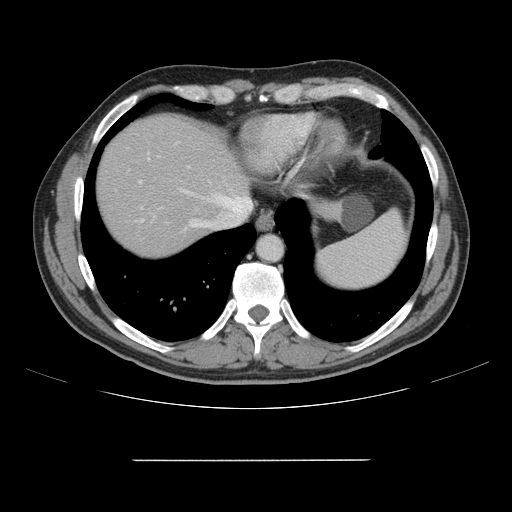
Contrast-enhanced abdominal CT, one axial slice; slice 135 of 164 in the series (ordered by position); intravenous contrast given; soft-tissue window (W 400 / L 40 HU); 2.5 mm slice thickness; 512 × 512 image matrix, field of view 404 × 404 mm. Male patient, age 54 years. Case-level facts recorded for this patient, not image findings: diagnosis: colorectal cancer liver metastases, imaged before liver resection; multiple liver metastases: yes; largest metastasis: 1 cm; disease in both lobes: no.
Annotated regions visible in this slice (outlined manually by an expert reader):
- hepatic veins: box from (x=180, y=189) to (x=252, y=228) px
- liver: (x=98, y=117)–(x=247, y=257)
- planned liver remnant (the part of the liver to remain after resection): (x=97, y=117)–(x=245, y=257)
- portal vein (with intrahepatic branches): (x=139, y=143)–(x=177, y=183)